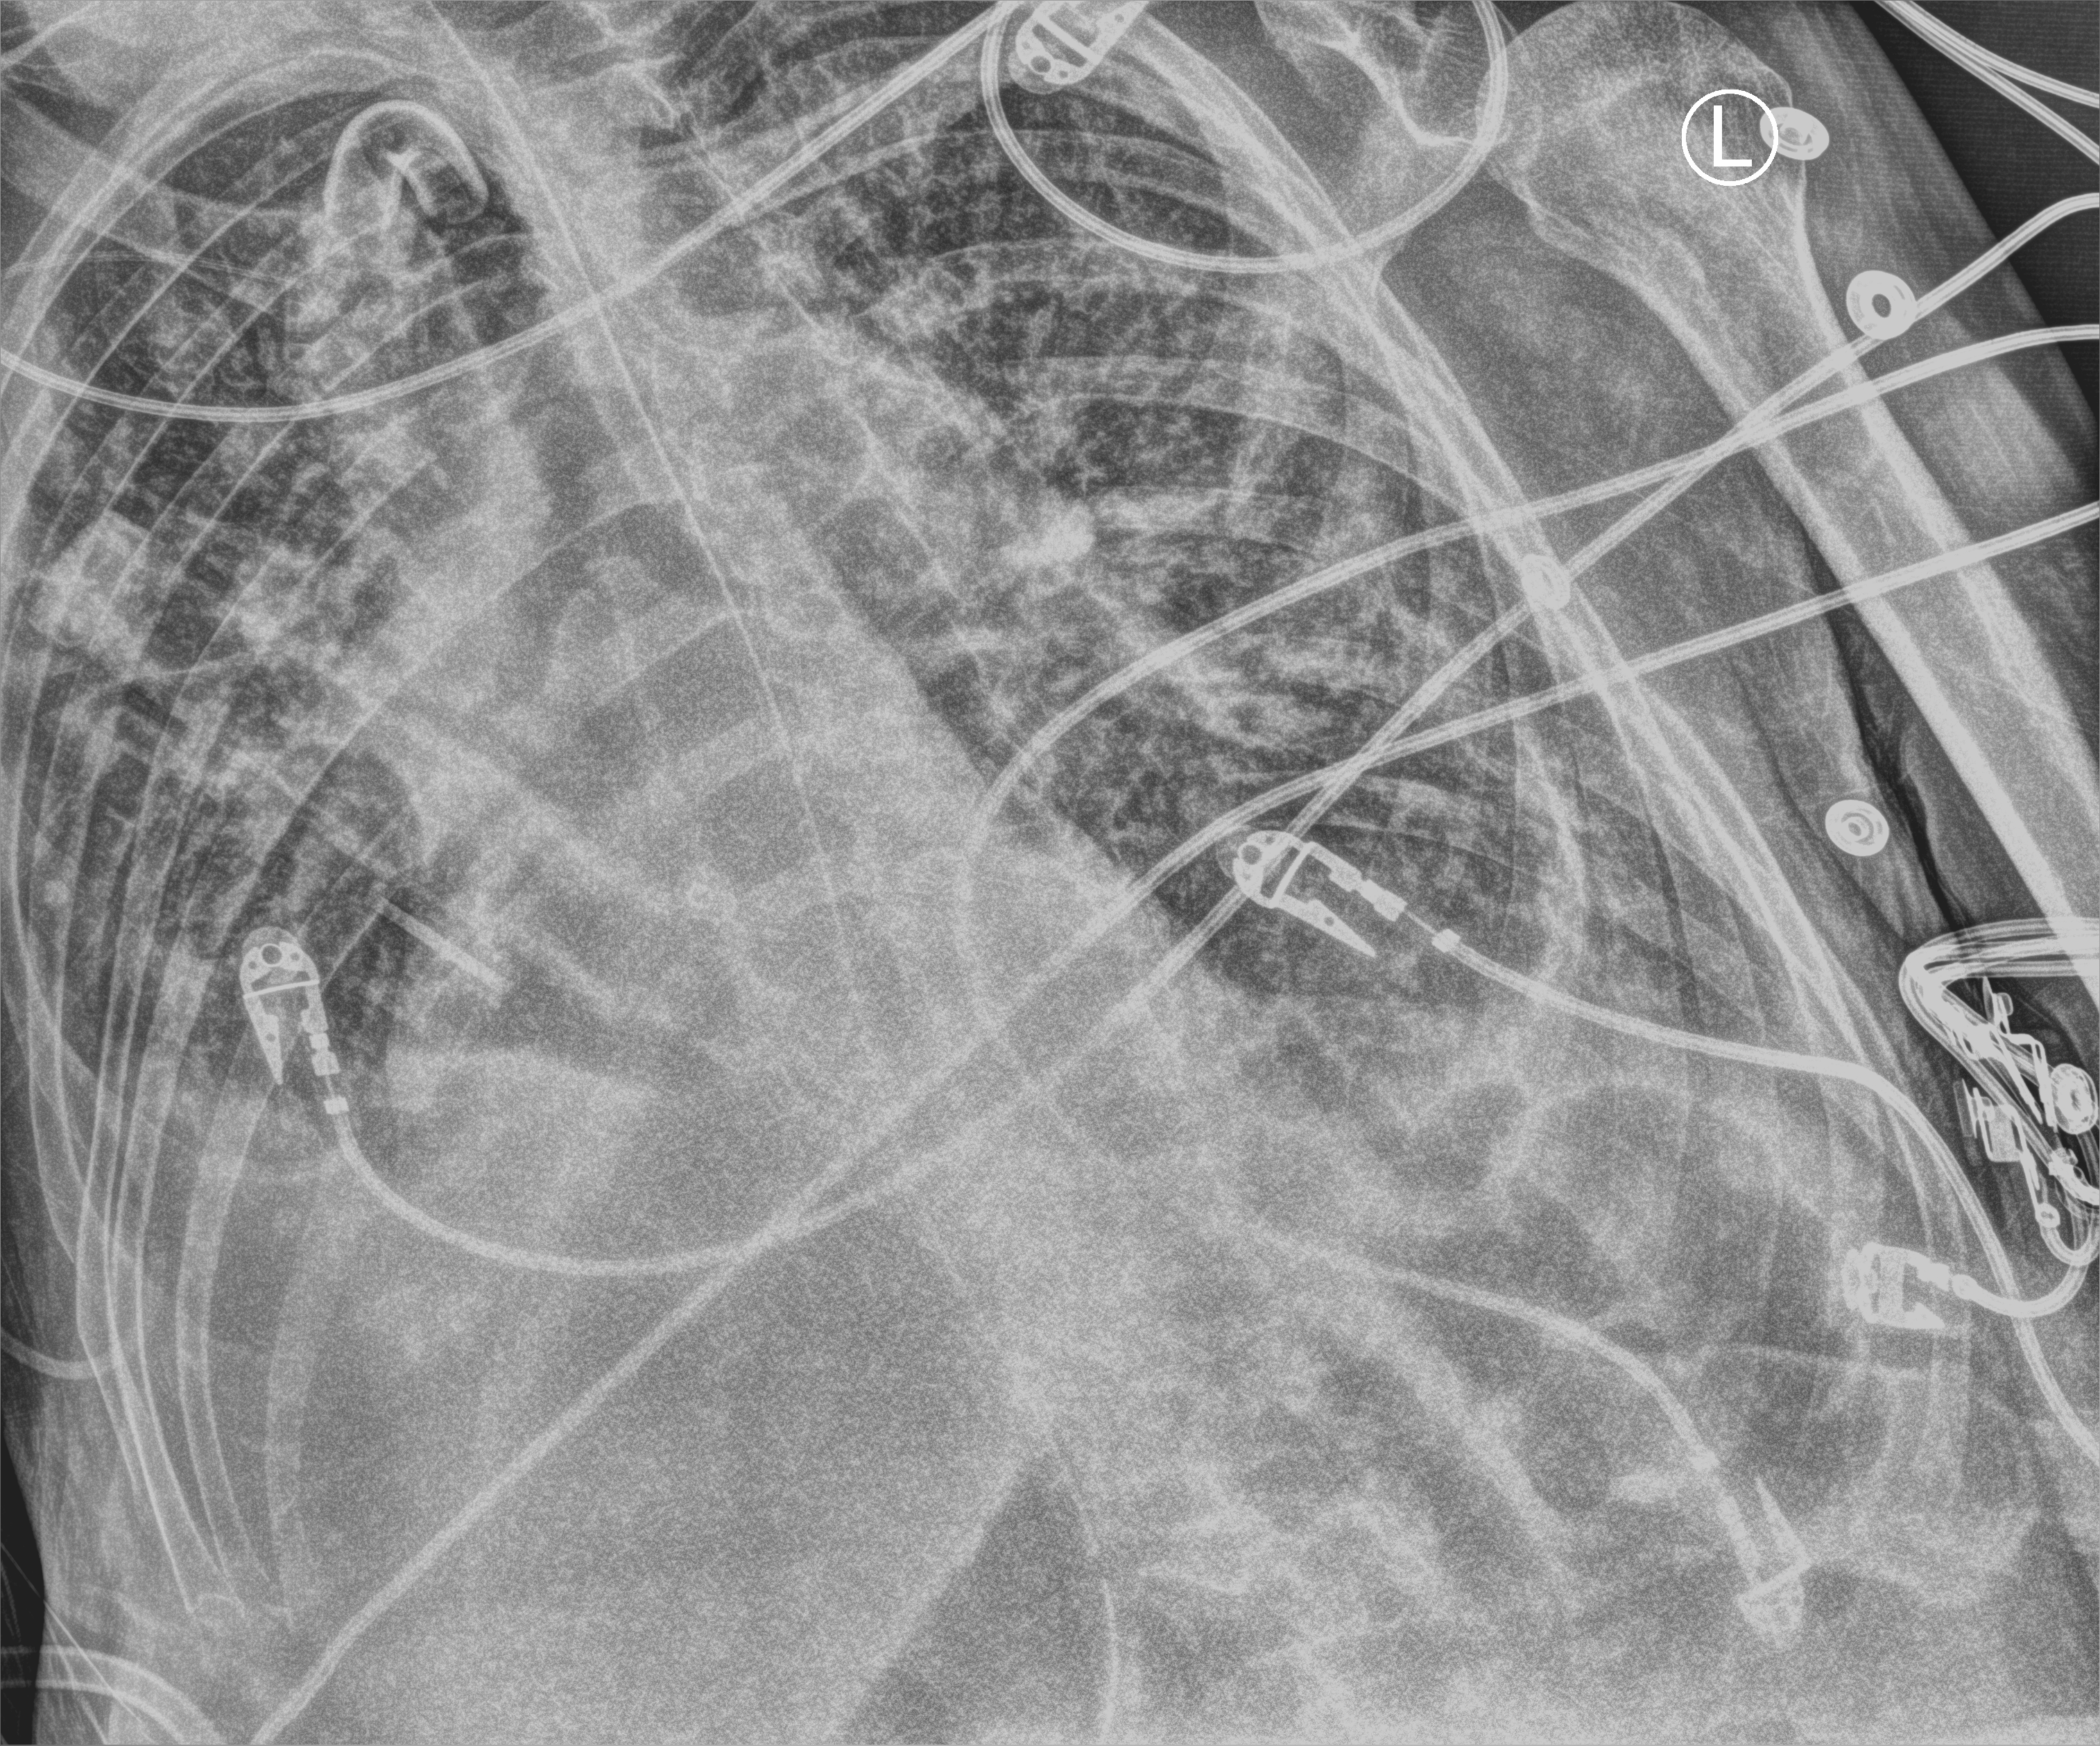
Chest X-ray (portable); anteroposterior (AP) projection. Male patient hospitalised with COVID-19, age 75–90 years.
Admission-level facts for this patient (not findings on this image; timing relative to this image not recorded): chronic kidney disease (admission record): no; length of hospital stay: 70 days.